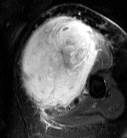
MRI of an extremity soft-tissue mass, one axial slice. Position 44 of 87 along the scan axis. T2-weighted fat-saturated. MR volume resampled by the dataset authors to the PET/CT grid (not the native acquisition matrix). 3.27 mm slice thickness. 127 × 138 image matrix, field of view 124 × 135 mm. Female patient. From the clinical record (not read from this slice): histological type: pleiomorphic leiomyosarcoma; grade: high; site of the primary tumour: left biceps.
Structures marked on this image (expert contour drawn on MRI and transferred to this co-registered scan by the dataset authors):
- gross tumour volume including surrounding oedema: box from (x=20, y=16) to (x=105, y=113) px
- gross tumour volume (mass): (x=20, y=16)–(x=98, y=108)